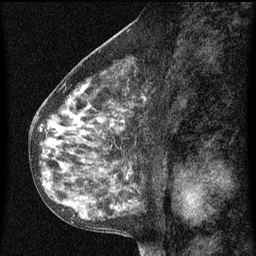
Breast MRI (dynamic contrast-enhanced), one sagittal slice. Slice 38 of 60 in the series (ordered by position). Dynamic contrast-enhanced series, image 2 of 3 at this slice position (ordered by acquisition). 1.5 T. TE 4.2 ms, TR 8 ms. 256 × 256 image matrix. Female patient, age 55 years.
Annotated regions visible in this slice (semi-automatically segmented with operator editing):
- analysis volume of interest (the breast-tissue region the enhancement analysis was run in; not a lesion): bounding box (x1, y1, x2, y2) in pixels: (34, 68, 151, 151)
- tumour enhancement mask (voxels above the 70 % enhancement threshold inside the analysis volume of interest): (40, 84, 145, 137)